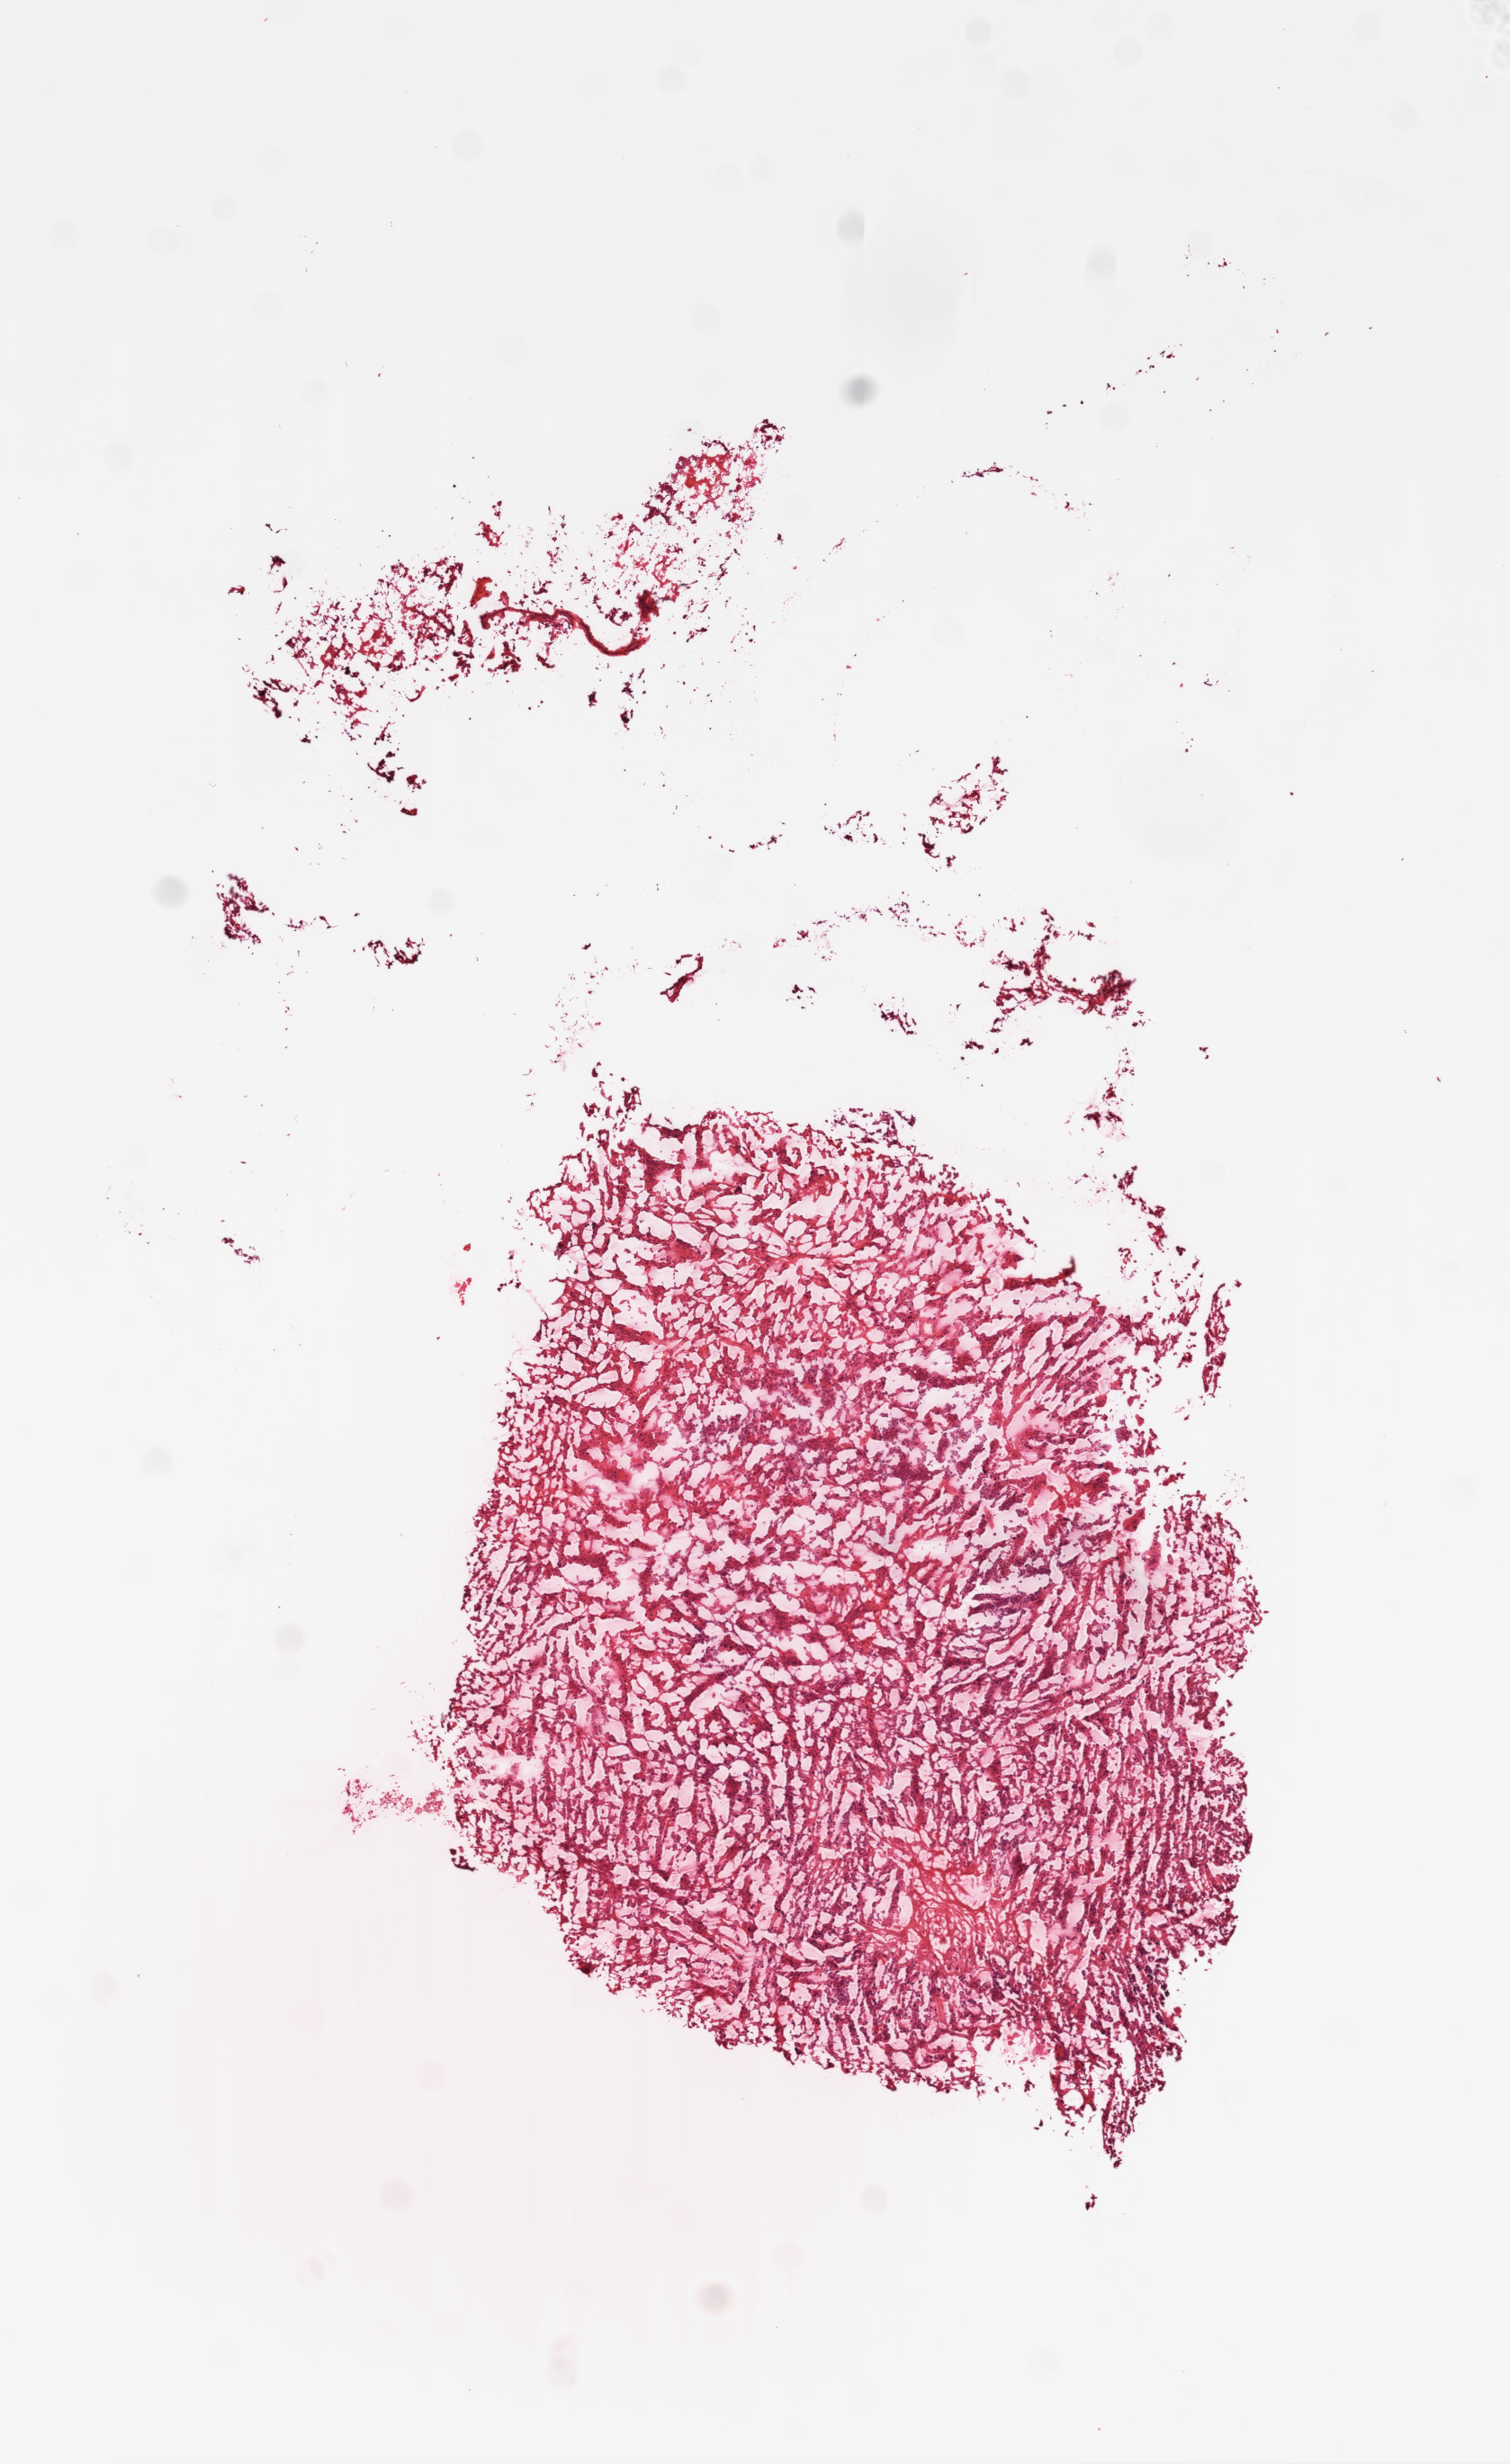
Hematoxylin and eosin (H&E) stained whole-slide image — a low-resolution overview of the entire scanned area, about 6.8 x 11.0 mm (slide scanned at 20x). Frozen section from the top of the tissue portion. Brain, primary tumour sample. Patient: male, age at initial diagnosis 58 years. Pathologist review of this section (percent, as recorded): tumour cells 80%, tumour nuclei 85%, normal cells 10%, stromal cells 10%, necrosis 0%.
Histologic diagnosis: Glioblastoma.